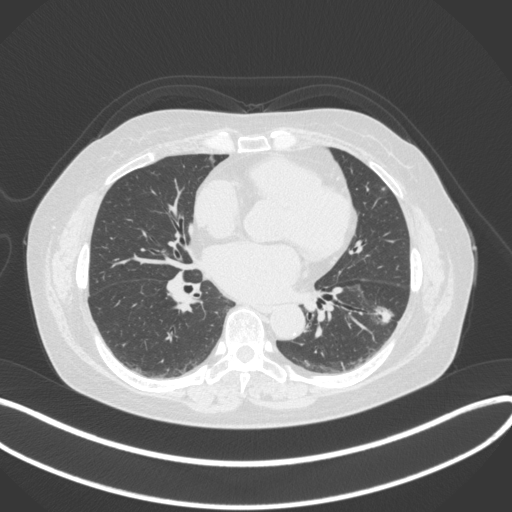
Chest CT, one axial slice; position 165 of 373 along the scan axis; reconstruction kernel B31f; 120 kVp; lung window (W 1500 / L -600 HU); 1 mm slice thickness; 512 × 512 image matrix, field of view 400 × 400 mm. Patient: female, 67 years. Case-level facts recorded for this patient, not image findings: clinical TNM (as recorded): T1c N0 M0; histopathological grade: G2.
Annotated regions visible in this slice (rectangle marked by the reading radiologist):
- lung tumour (recorded histology: adenocarcinoma): bounding box [x1, y1, x2, y2] px = [362, 296, 399, 332]